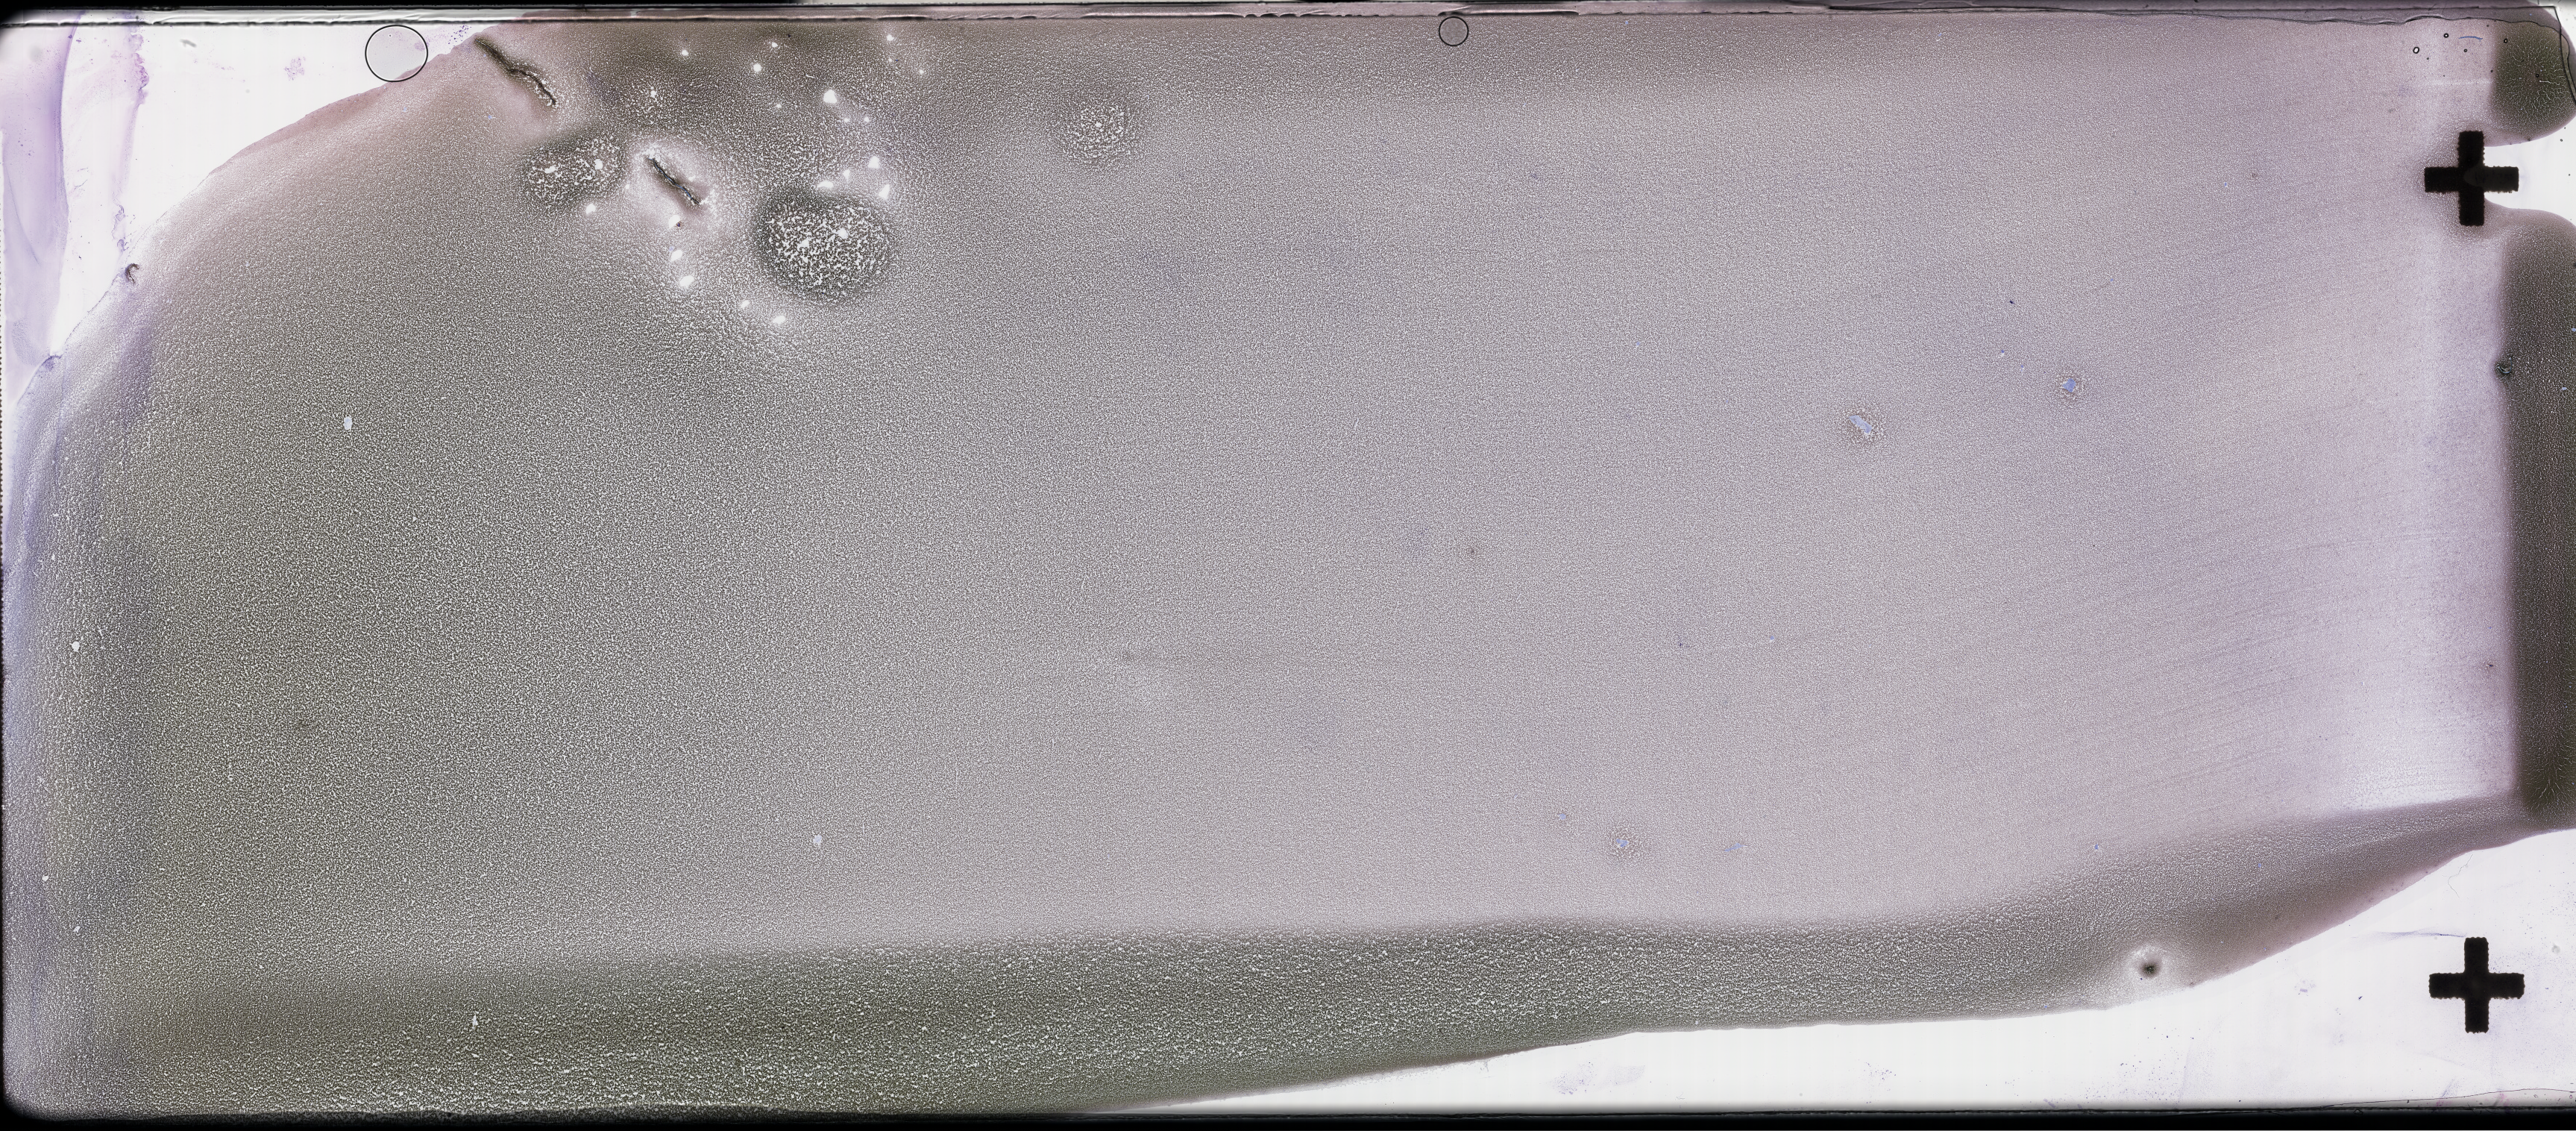
Wright-Giemsa-stained whole blood smear, whole-slide image, low-resolution overview of the scanned area, about 55.8 x 24.5 mm, collected on treatment. Patient sex: female.
* patient diagnosis: Plasma Cell Myeloma